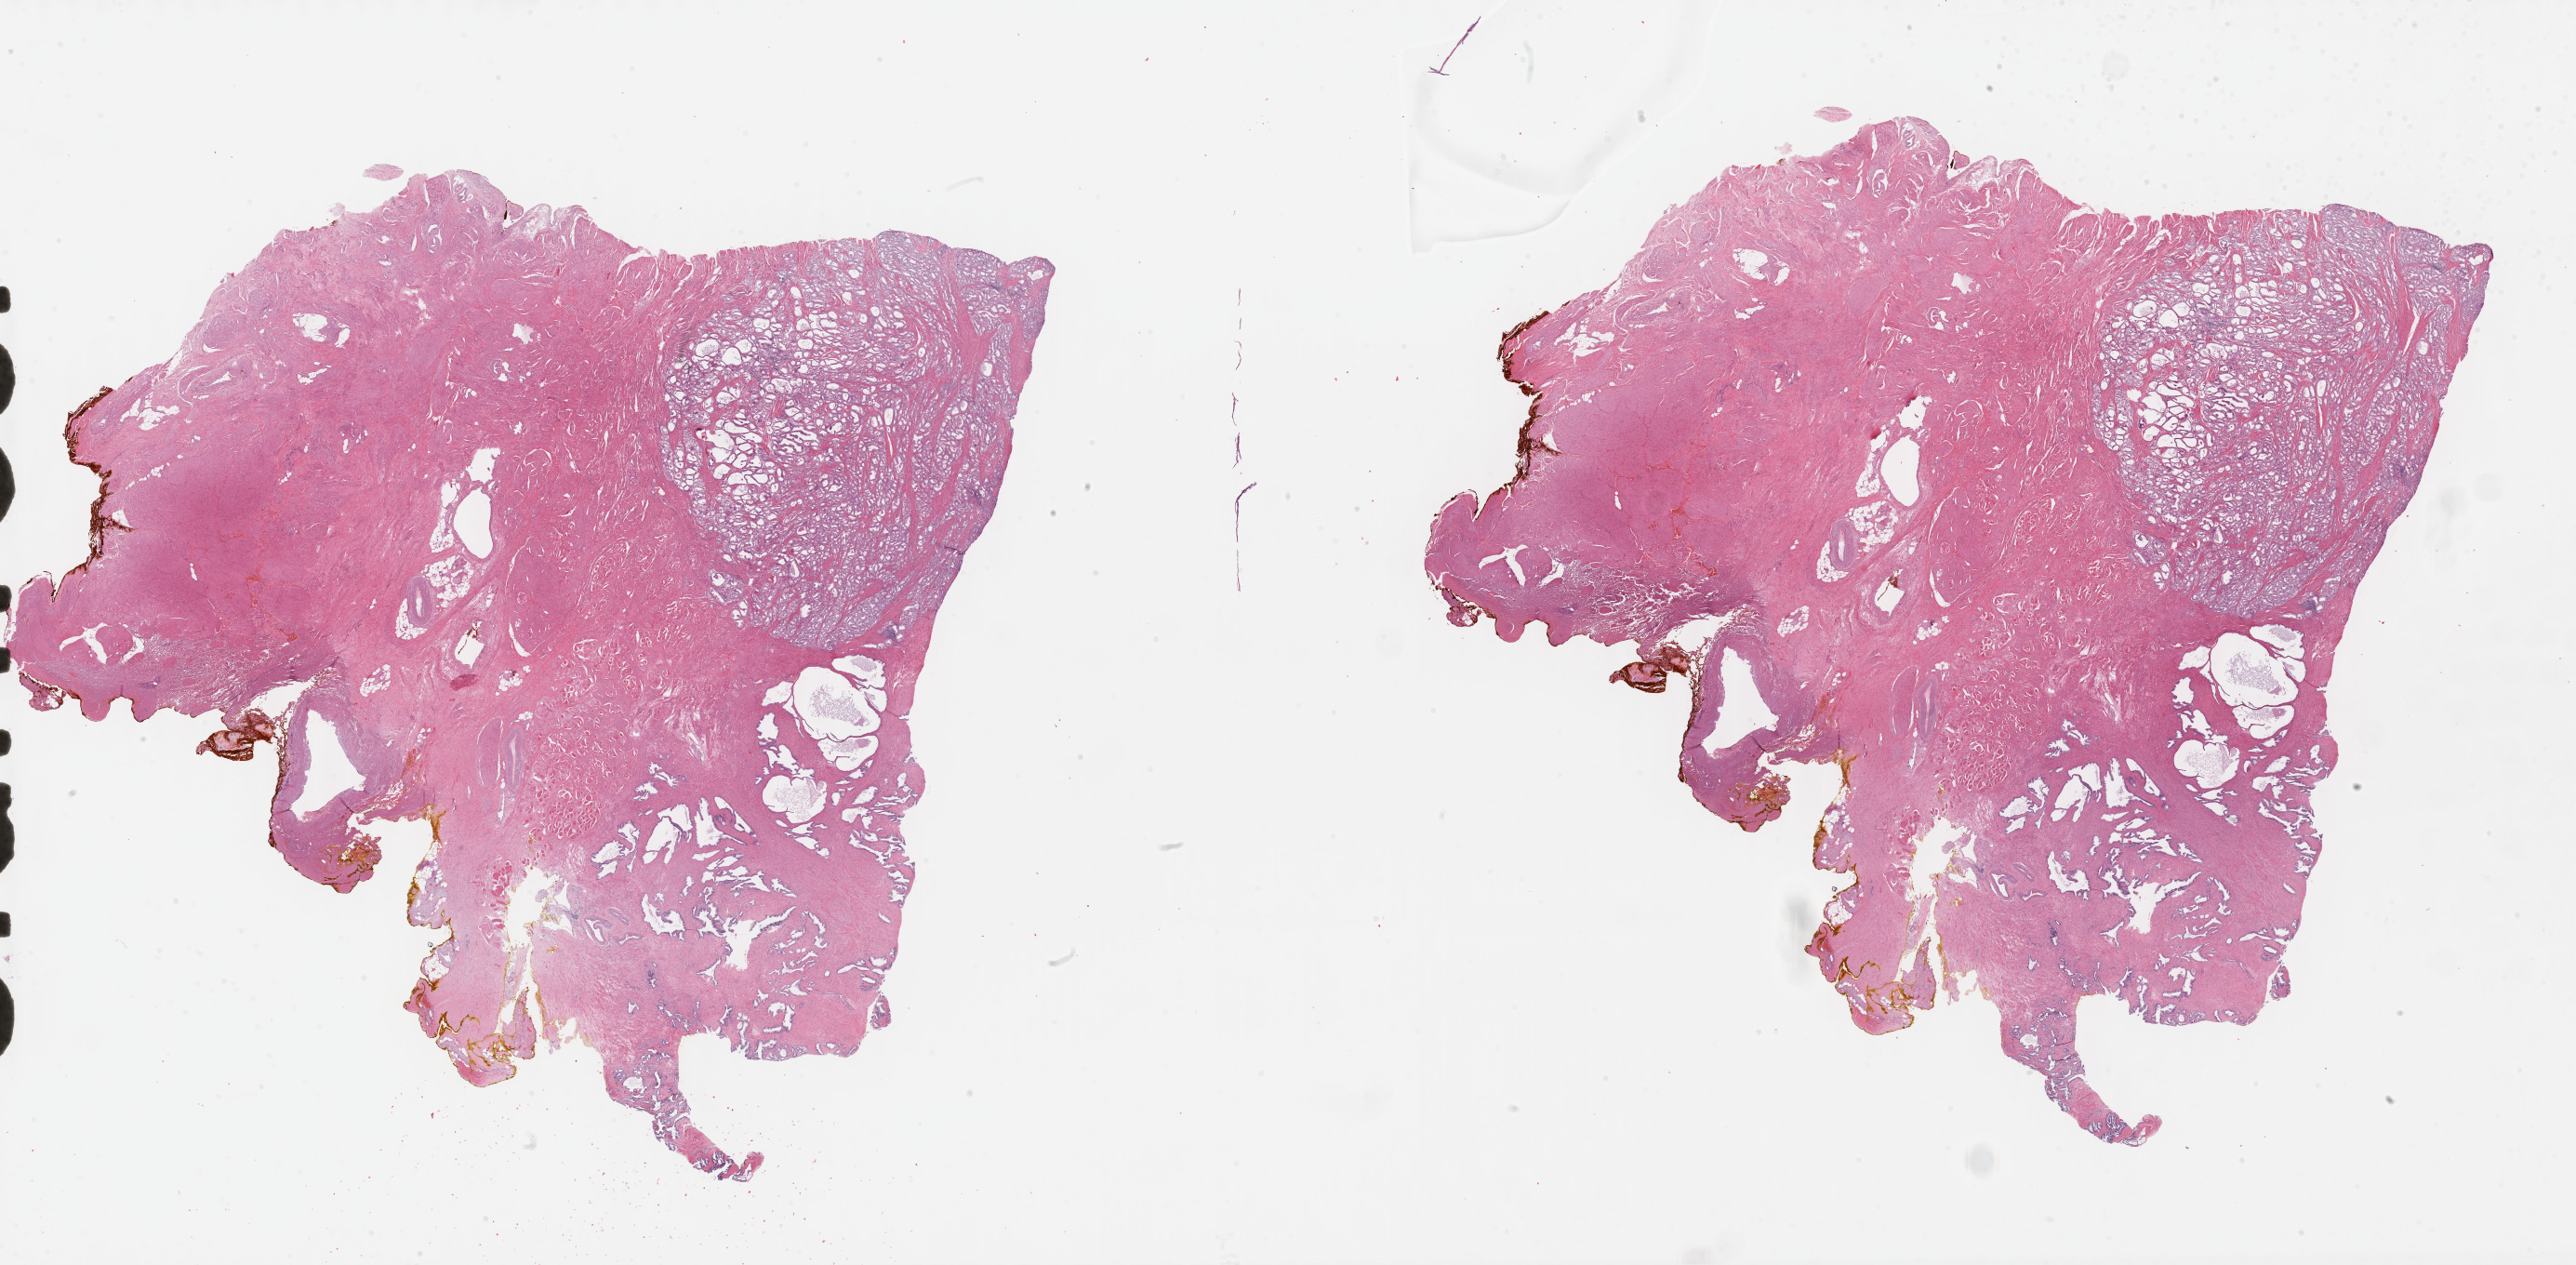
Whole-slide histology image, H&E-stained, low-resolution overview of the scanned area, about 44.8 x 22.0 mm (slide scanned at 40x). FFPE section. Prostate, primary tumour sample. Male patient; age at initial diagnosis 59 years. Gleason score: 6 (3+3).
* histologic diagnosis: Adenocarcinoma, NOS